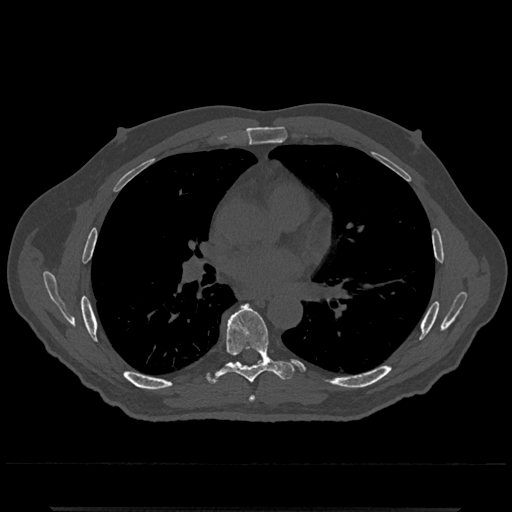
CT including the spine, one axial slice. Position 722 of 797 along the scan axis. Reconstruction kernel Br40s/3. 120 kVp. Bone window (W 1800 / L 400 HU). 0.5 mm slice thickness. 512 × 512 image matrix, field of view 393 × 393 mm. Patient: male, 67 years. Case-level facts recorded for this patient, not image findings: primary cancer: prostate.
Annotated regions visible in this slice (semi-automatic segmentation, software-assisted and operator-edited):
- T6 vertebra: box from (x=249, y=396) to (x=256, y=402) px
- T7 vertebra: (x=219, y=304)–(x=293, y=383)